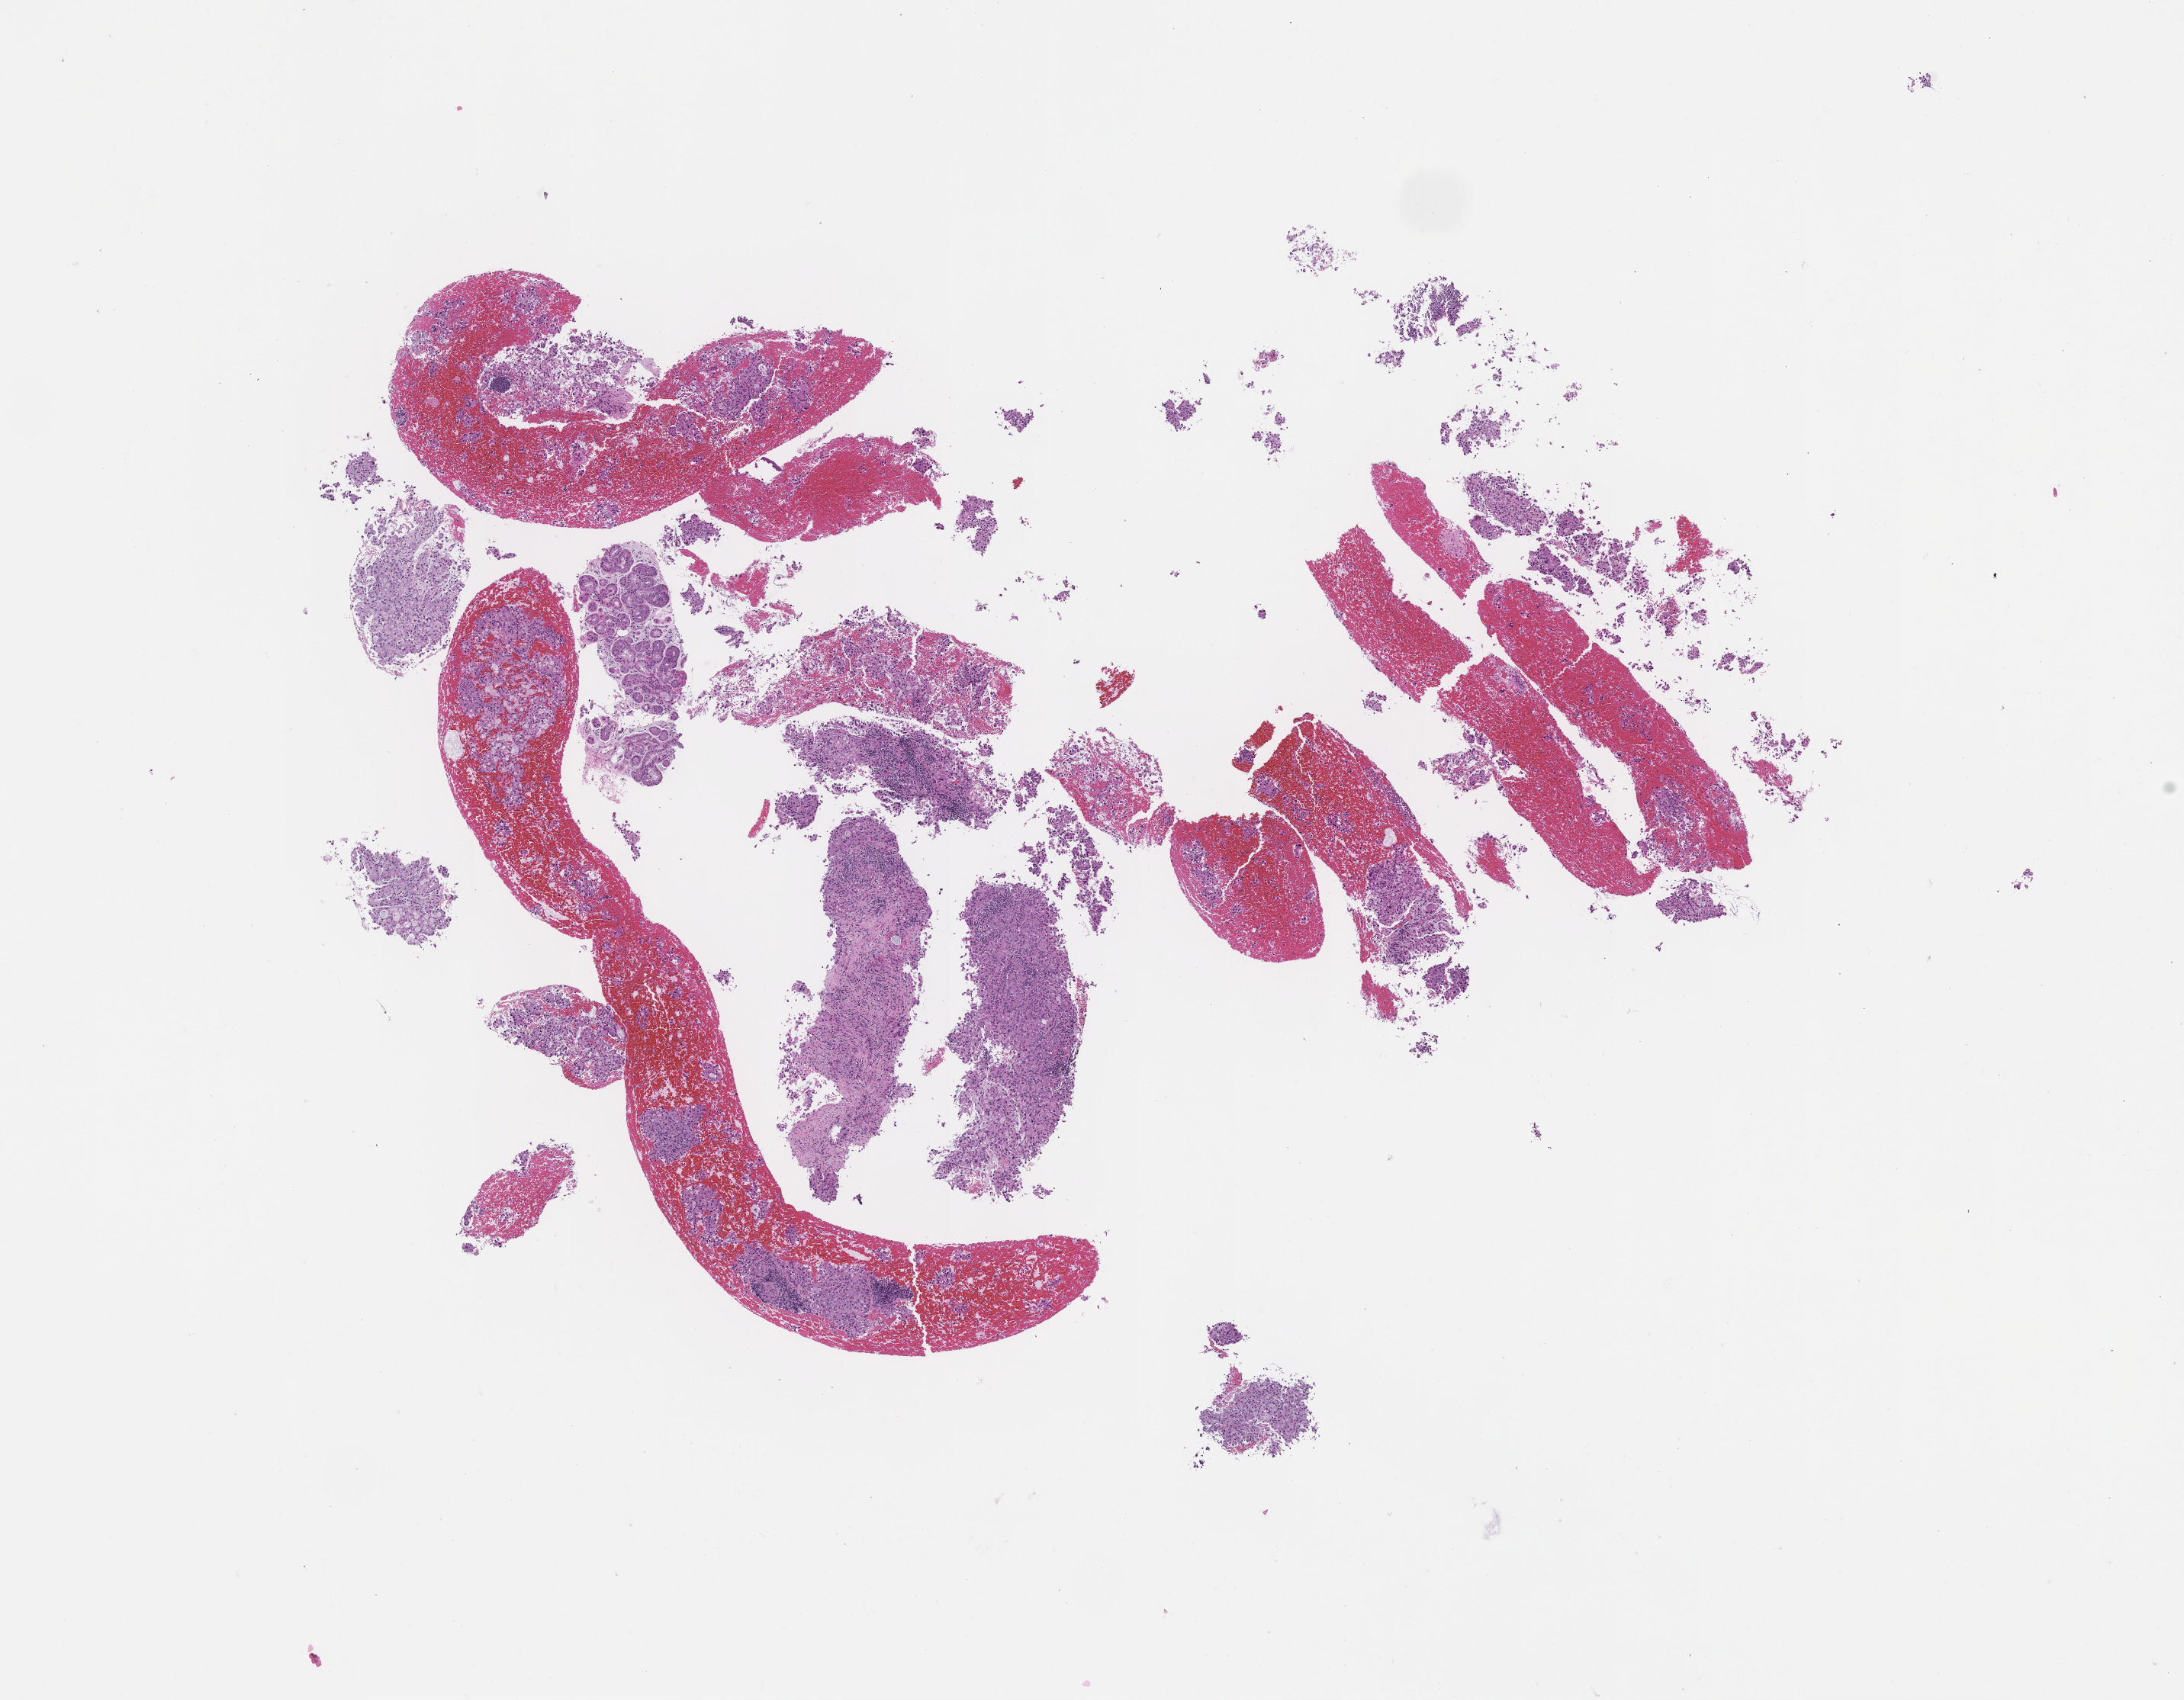
Digitized haematoxylin and eosin-stained section — whole scanned area (about 11.6 x 9.0 mm) shown as a low-resolution overview; formalin-fixed paraffin-embedded section. Male patient.
This section: metastasis (sampled organ not recorded). Primary diagnosis of the patient: Non-Small Cell Lung Carcinoma.